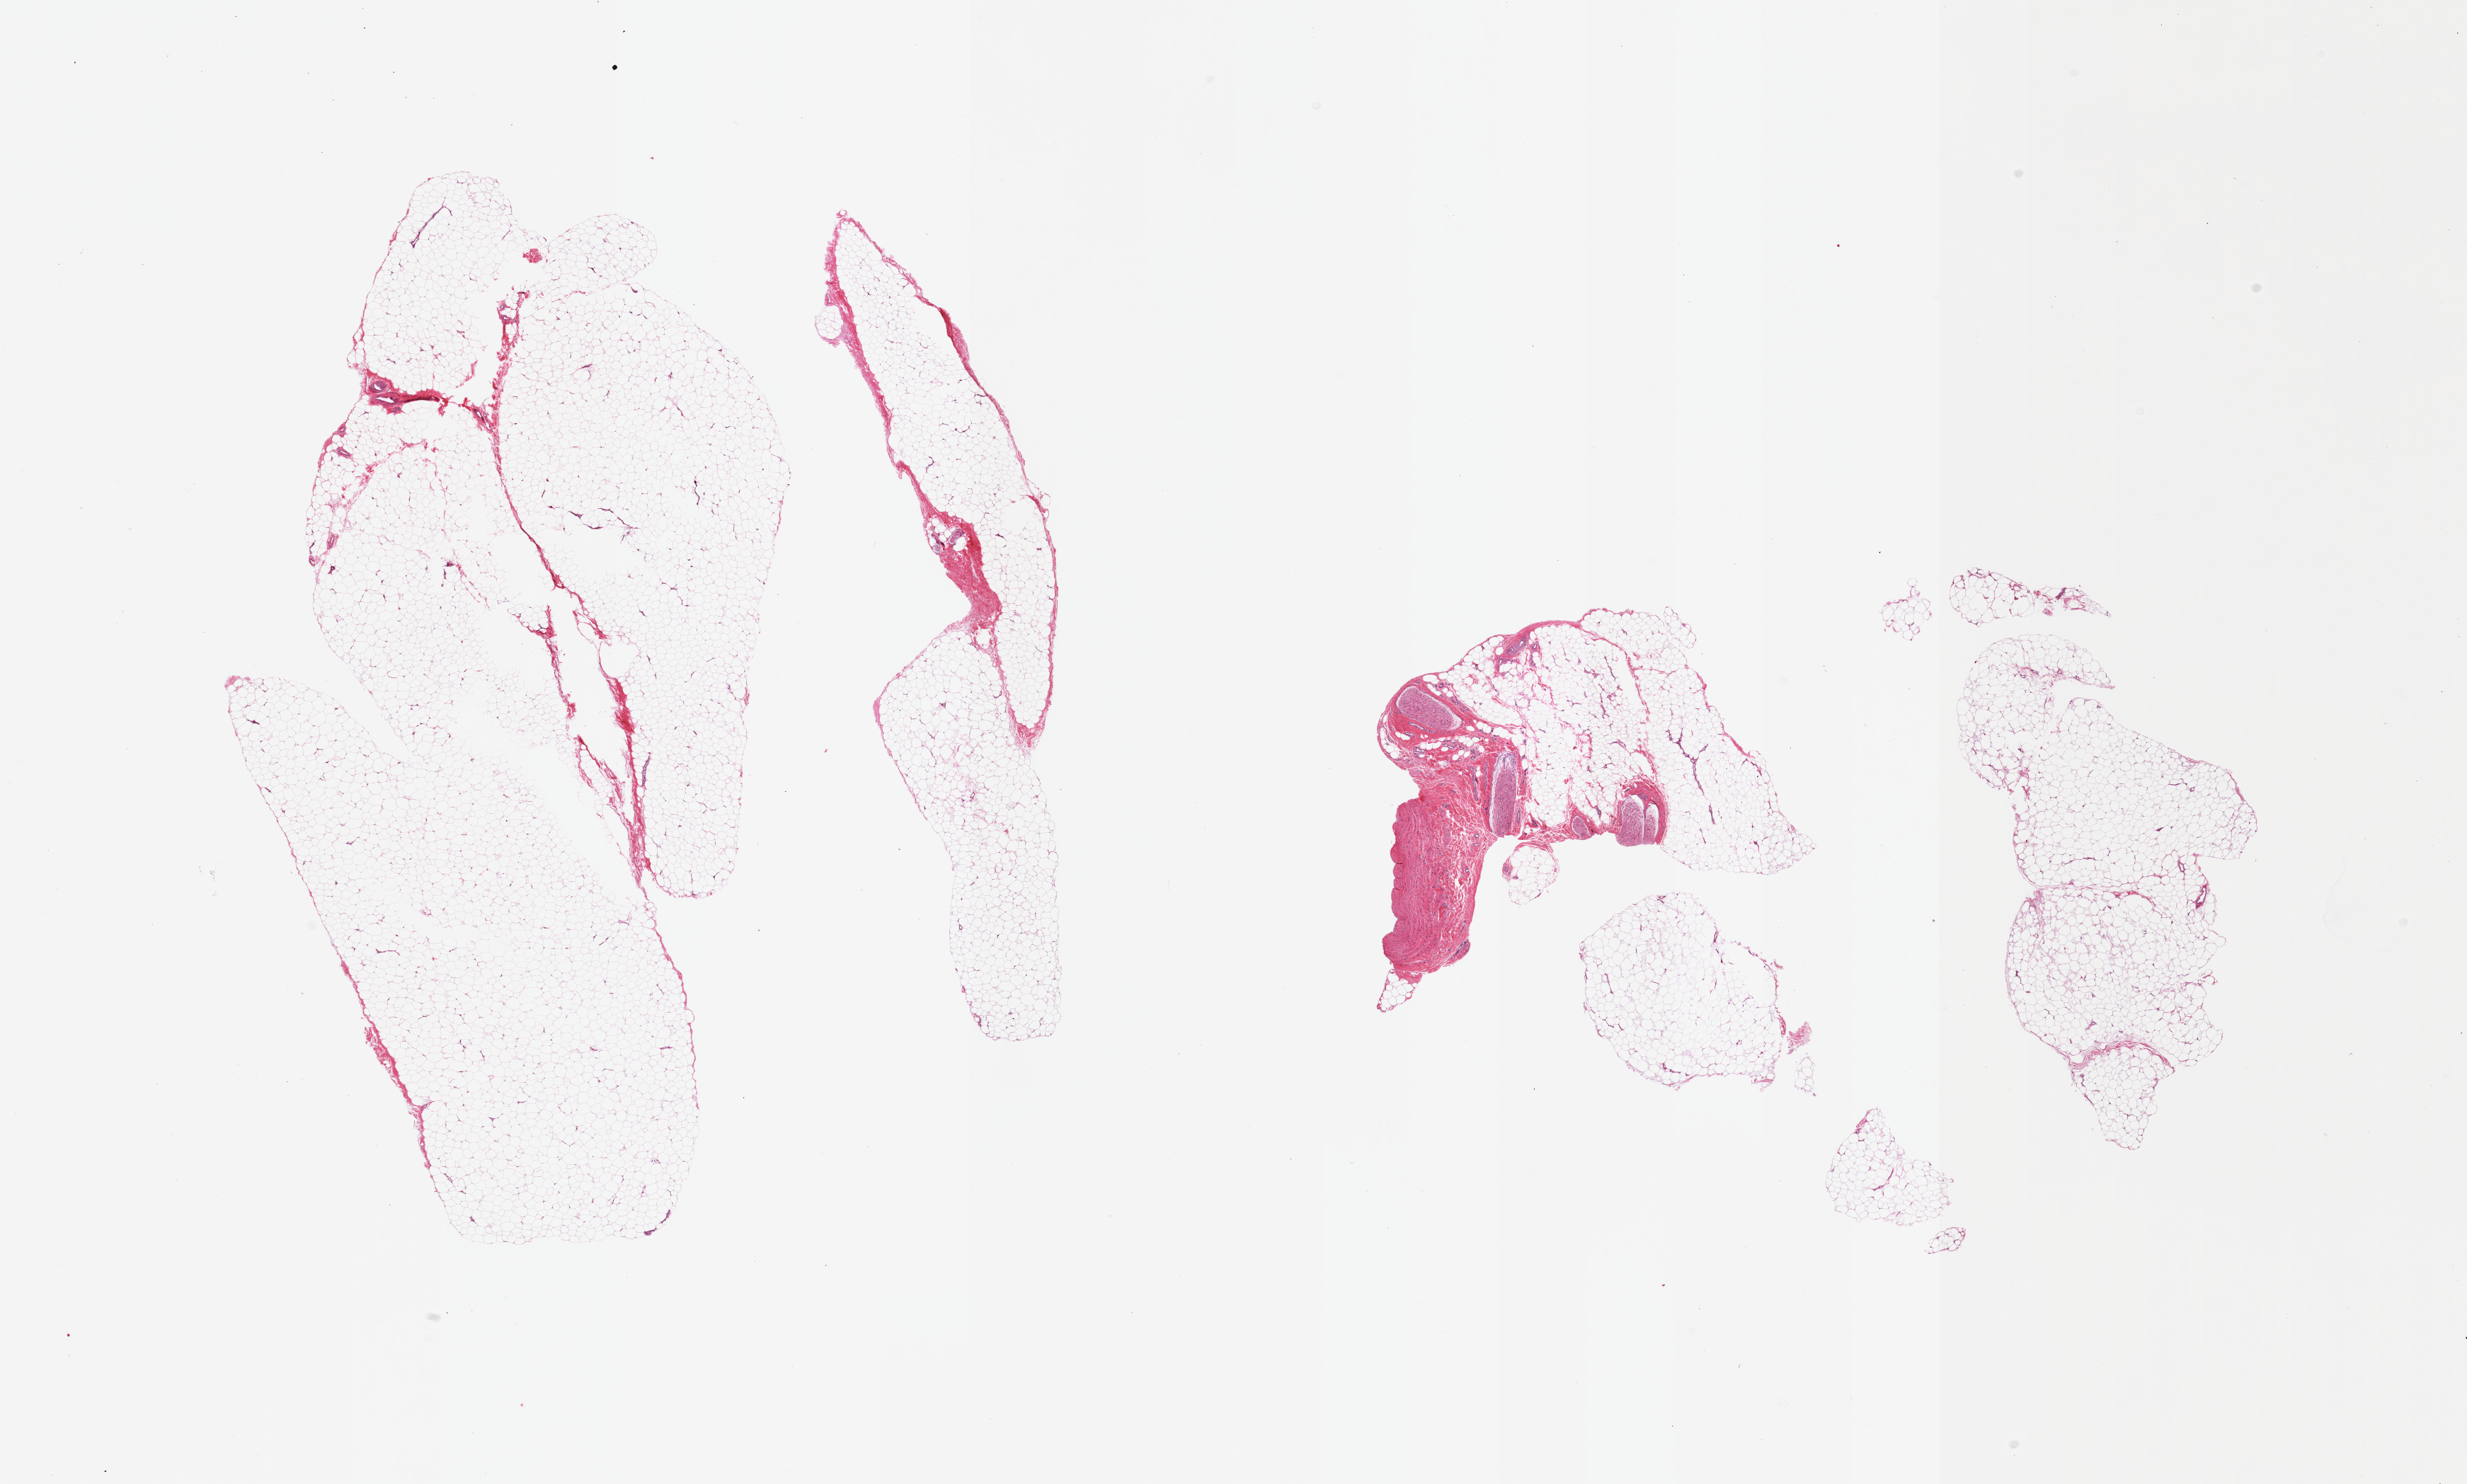
Digitized hematoxylin and eosin (H&E)-stained section, whole scanned area (about 27.6 x 16.6 mm, acquisition: 20x scan) shown as a low-resolution overview, PAXgene-fixed paraffin-embedded (PFPE) section, section of adipose tissue (target tissue), donor tissue sample.
Review note (as recorded): 2 pieces, ~5-10% adherent fascia/peripheral nerve elements.